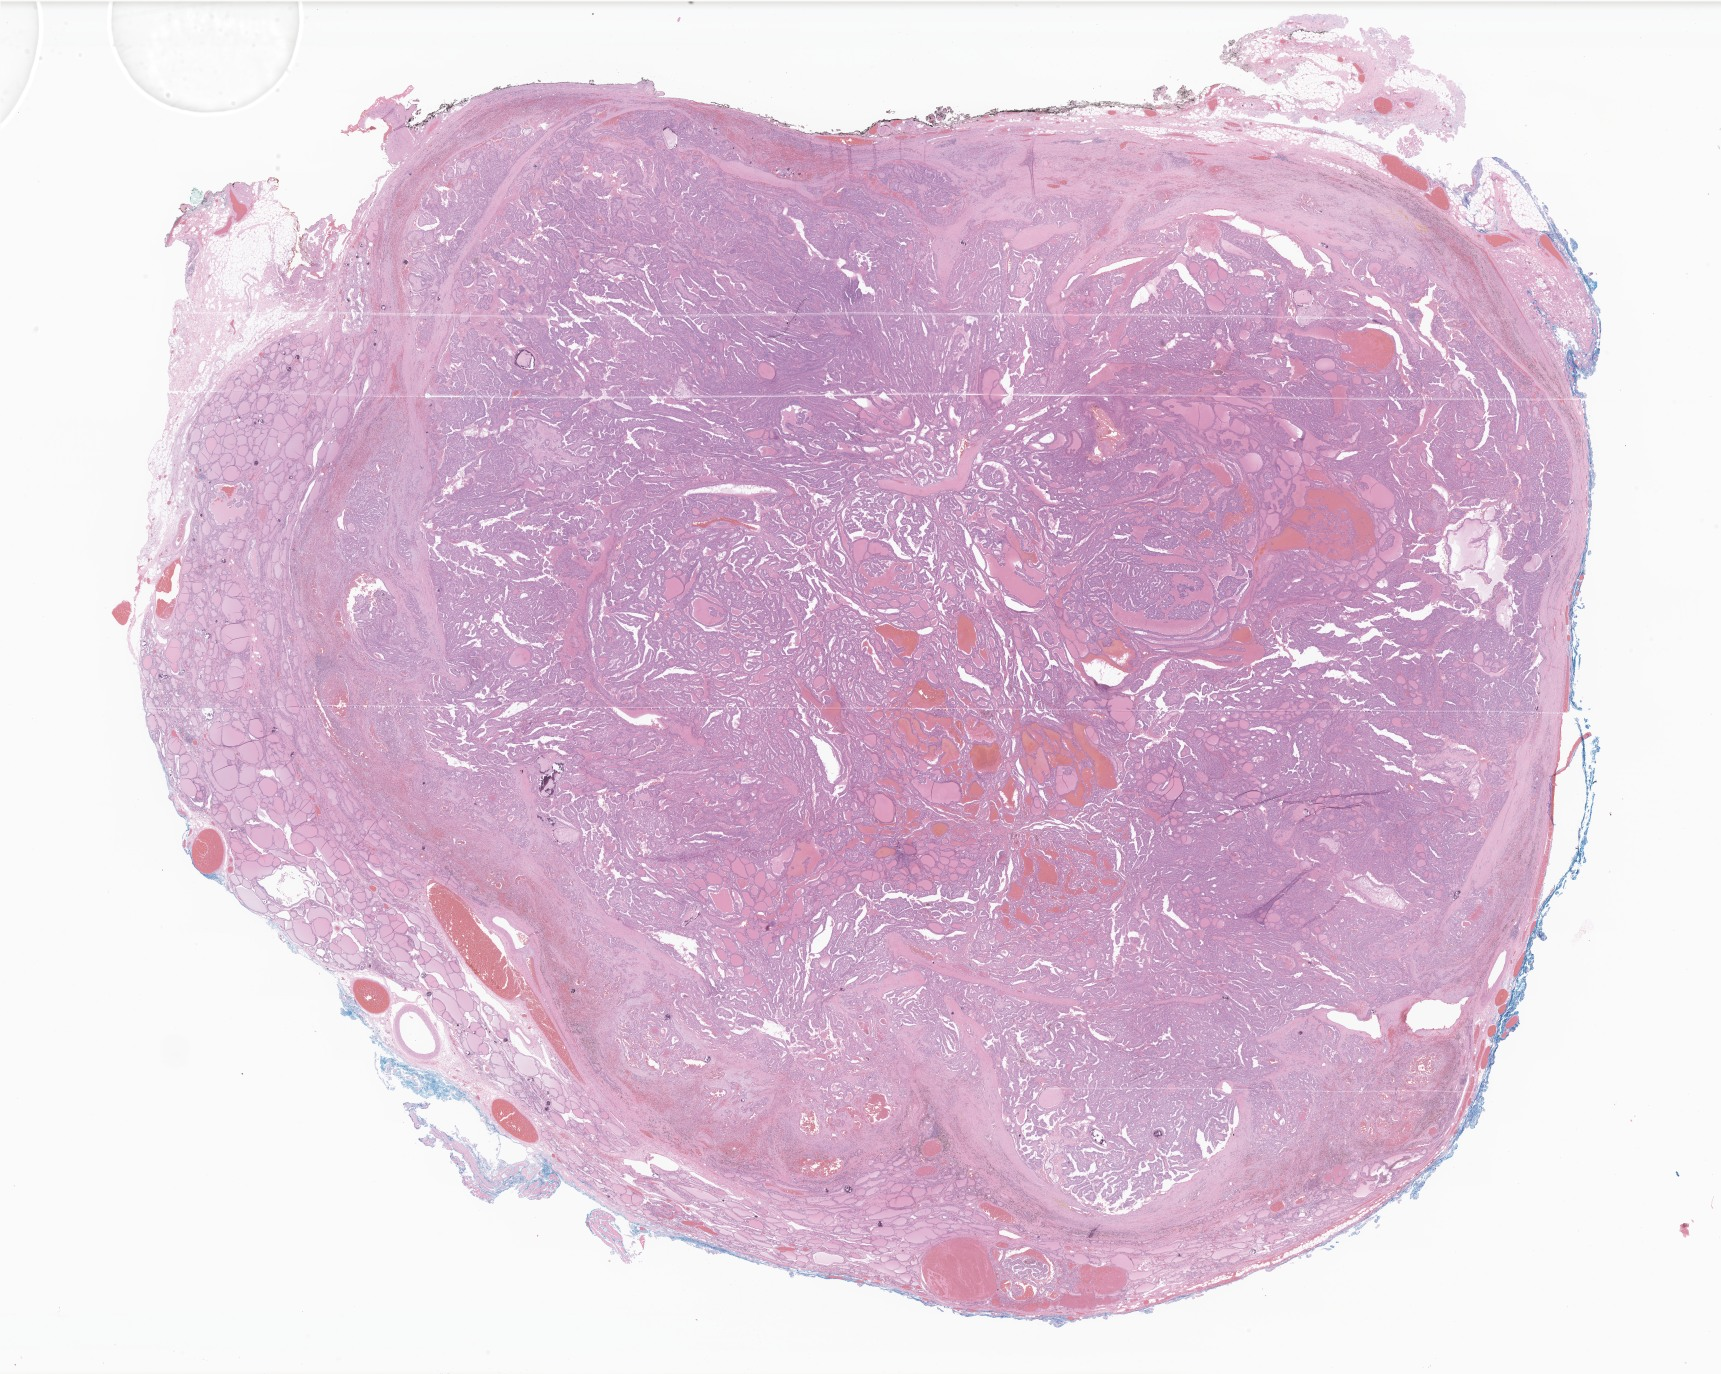
Hematoxylin and eosin (H&E) whole-slide image of tumor tissue from the thyroid, a low-resolution overview of the entire scanned area, about 29.0 x 23.2 mm. FFPE section. Patient: female, age 200 months (16 years 8 months).
Diagnosis (ICD-O-3 morphology term): Carcinoma, NOS.